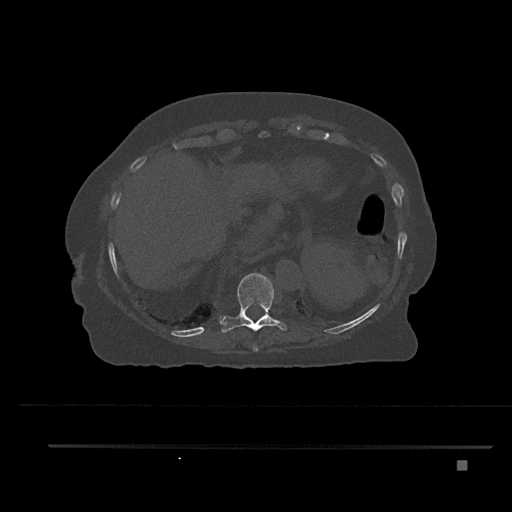
CT including the spine, one axial slice; slice 356 of 797 in the series (ordered by position); reconstruction kernel Br40s/3; bone window (W 1800 / L 400 HU); 0.5 mm slice thickness; 512 × 512 image matrix, field of view 437 × 437 mm. Female patient, age 76 years. Case-level facts recorded for this patient, not image findings: primary cancer: lung; vertebrae with lytic lesions (as recorded): T11, L3.
Structures marked on this image (semi-automatic segmentation, software-assisted and operator-edited):
- T10 vertebra: bounding box <220,273,287,333> (left, top, right, bottom; pixels)
- T9 vertebra: <253,343,258,352>